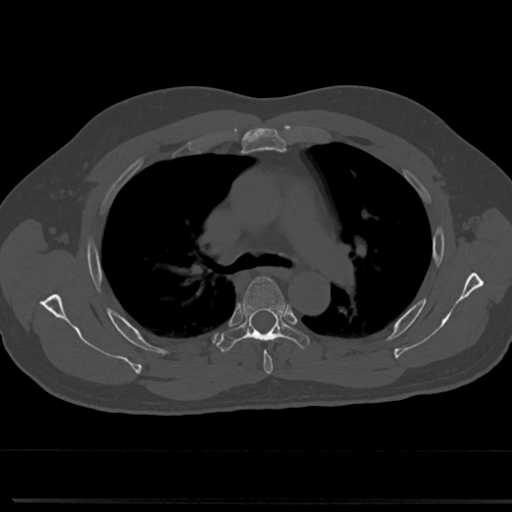
CT including the spine, one axial slice; slice 511 of 817 in the series (ordered by position); reconstruction kernel Br40s/3; 120 kVp; bone window (W 1800 / L 400 HU); 0.5 mm slice thickness; 512 × 512 image matrix, field of view 355 × 355 mm. Male patient, age 61 years. From the clinical record (not read from this slice): primary cancer: prostate.
Annotated regions visible in this slice (semi-automatic segmentation, software-assisted and operator-edited):
- T4 vertebra: bounding box (x1, y1, x2, y2) in pixels: (242, 285, 283, 373)
- T5 vertebra: (219, 276, 310, 352)